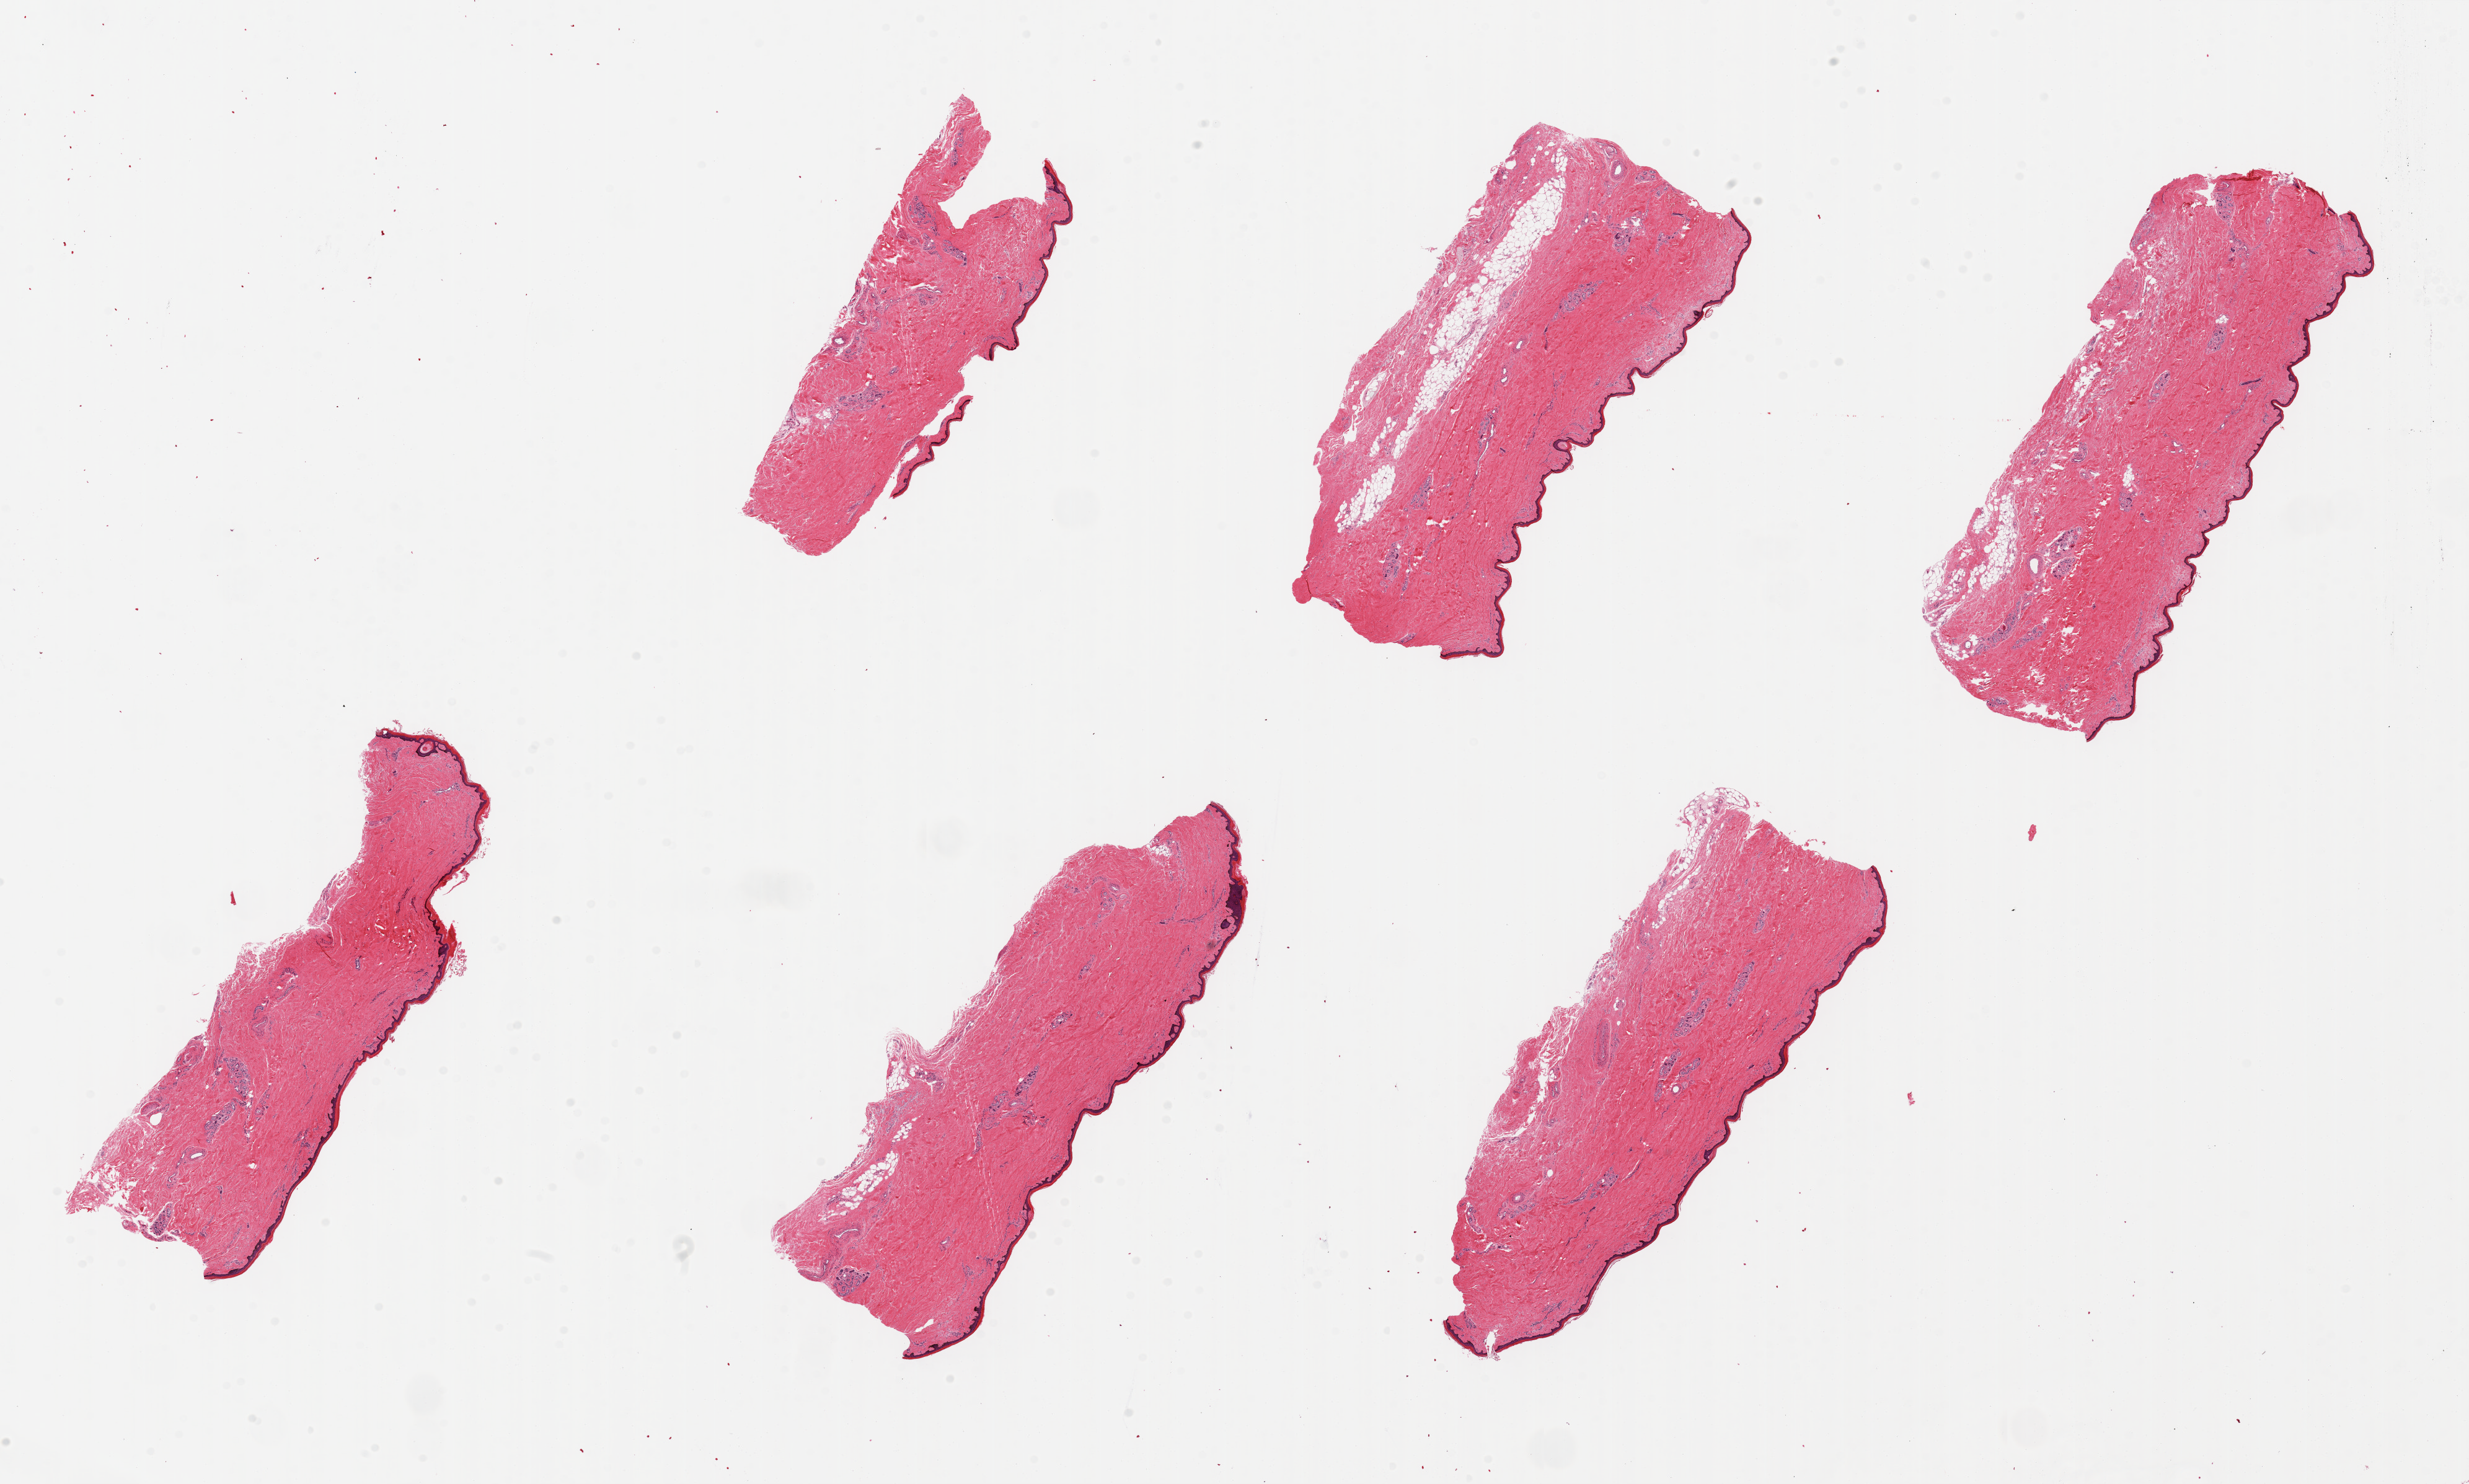
Haematoxylin and eosin whole-slide image — low-resolution overview of the scanned area, about 31.5 x 18.9 mm, PAXgene-fixed, paraffin-embedded tissue, sampled site (target tissue): skin of lower leg, tissue donor sample. Donor: male.
Review note (as recorded): 6 pieces, up to 8x3mm; Well trimmed, free of subcutaneous adipose.